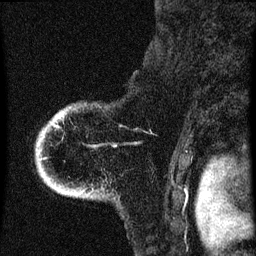
Breast MRI (dynamic contrast-enhanced), one sagittal slice. Slice 55 of 60 in the series (ordered by position). Dynamic contrast-enhanced series, image 2 of 4 at this slice position (ordered by acquisition). 1.5 T. TE 4.2 ms, TR 8 ms. 2 mm slice thickness. 256 × 256 image matrix, field of view 180 × 180 mm. Patient: female, 71 years.
Outlined on this slice (semi-automatic segmentation, software-assisted and operator-edited):
- analysis volume of interest (the breast-tissue region the enhancement analysis was run in; not a lesion): bounding box (x1, y1, x2, y2) in pixels: (35, 104, 116, 199)
- tumour enhancement mask (voxels above the 70 % enhancement threshold inside the analysis volume of interest): (59, 116, 61, 119)